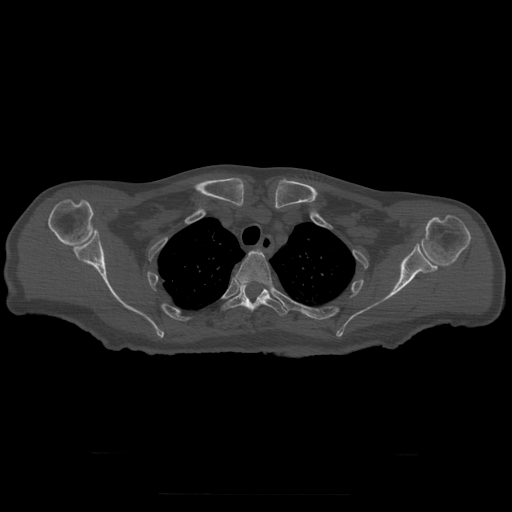
CT including the spine, one axial slice. Slice 250 of 397 in the series (ordered by position). Reconstruction kernel STANDARD. 120 kVp. Bone window (W 1800 / L 400 HU). 1.25 mm slice thickness. 512 × 512 image matrix, field of view 510 × 510 mm. Patient age 73 years. From the clinical record (not read from this slice): primary cancer: prostate.
Annotated regions visible in this slice (semi-automatic segmentation, software-assisted and operator-edited):
- T3 vertebra: bounding box (x1, y1, x2, y2) in pixels: (236, 250, 274, 295)
- T4 vertebra: (222, 284, 288, 315)